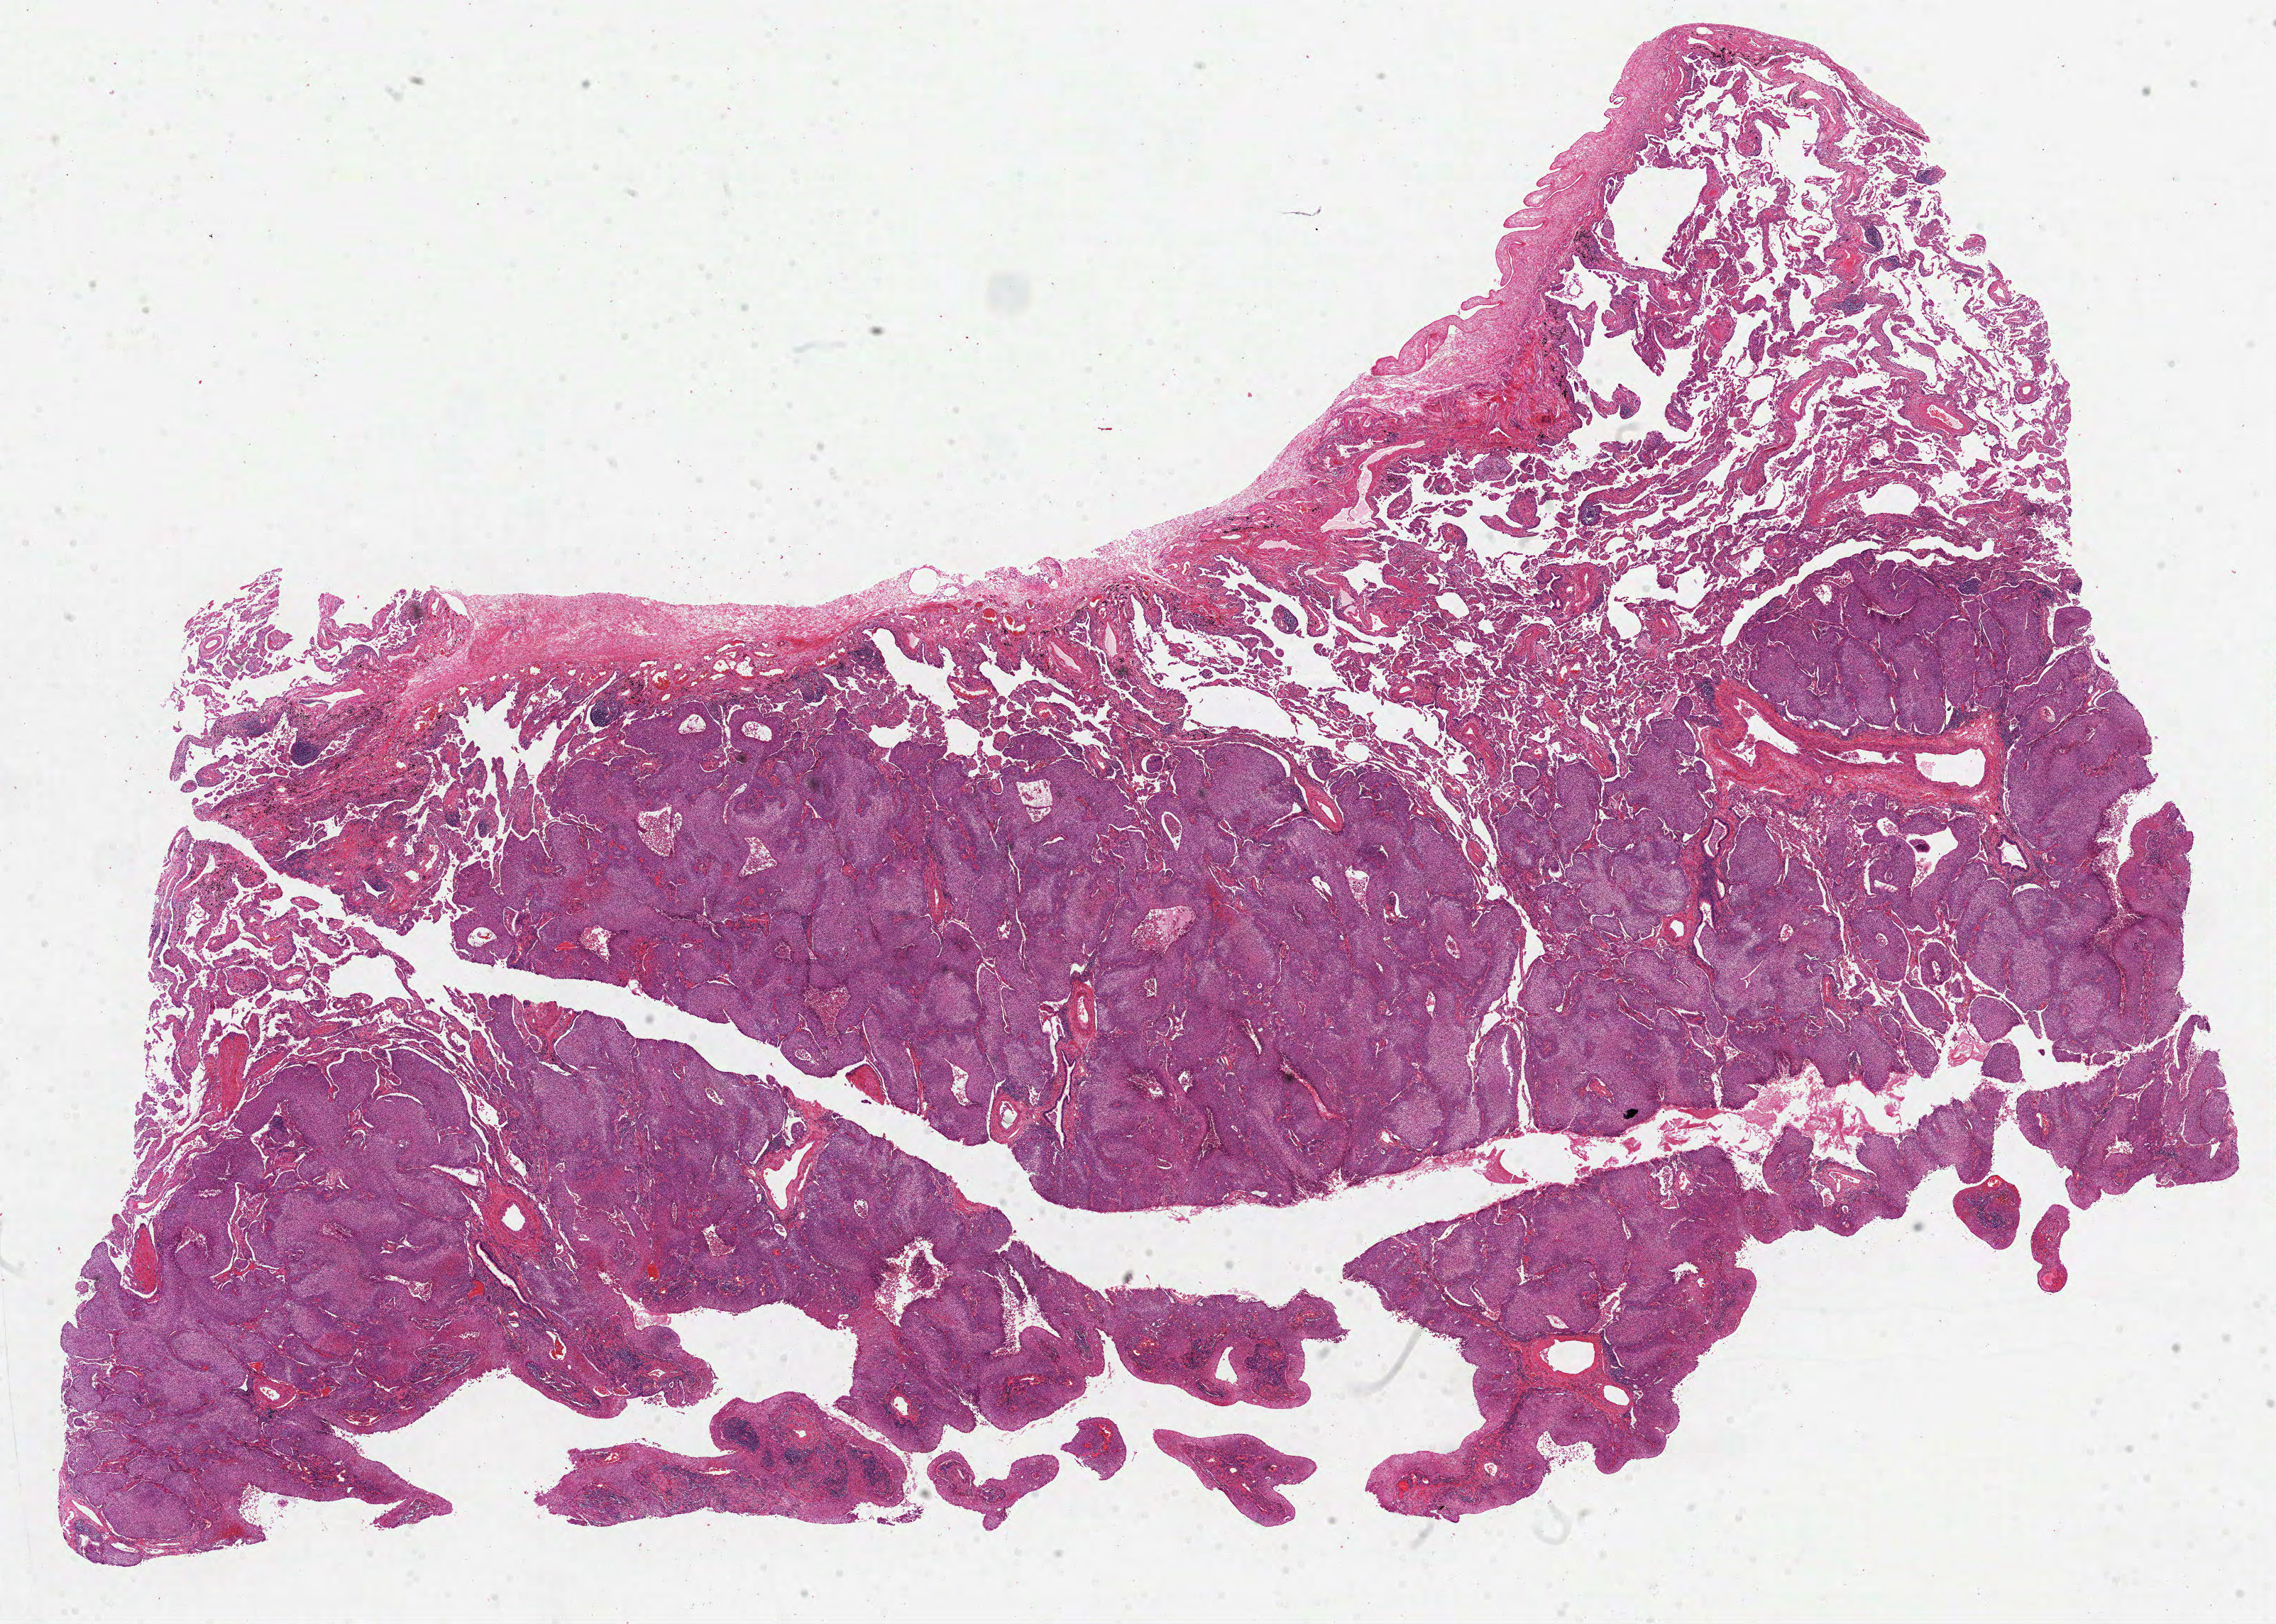
H&E whole-slide image — low-resolution overview of the scanned area, about 25.9 x 18.5 mm. FFPE section. Lung, primary tumour sample. Patient: male, age at initial diagnosis 74 years.
TNM: T3 N1 M0. Laterality: right. AJCC pathologic stage: IIIA. Histologic diagnosis: Squamous cell carcinoma, NOS (lower lobe, lung).